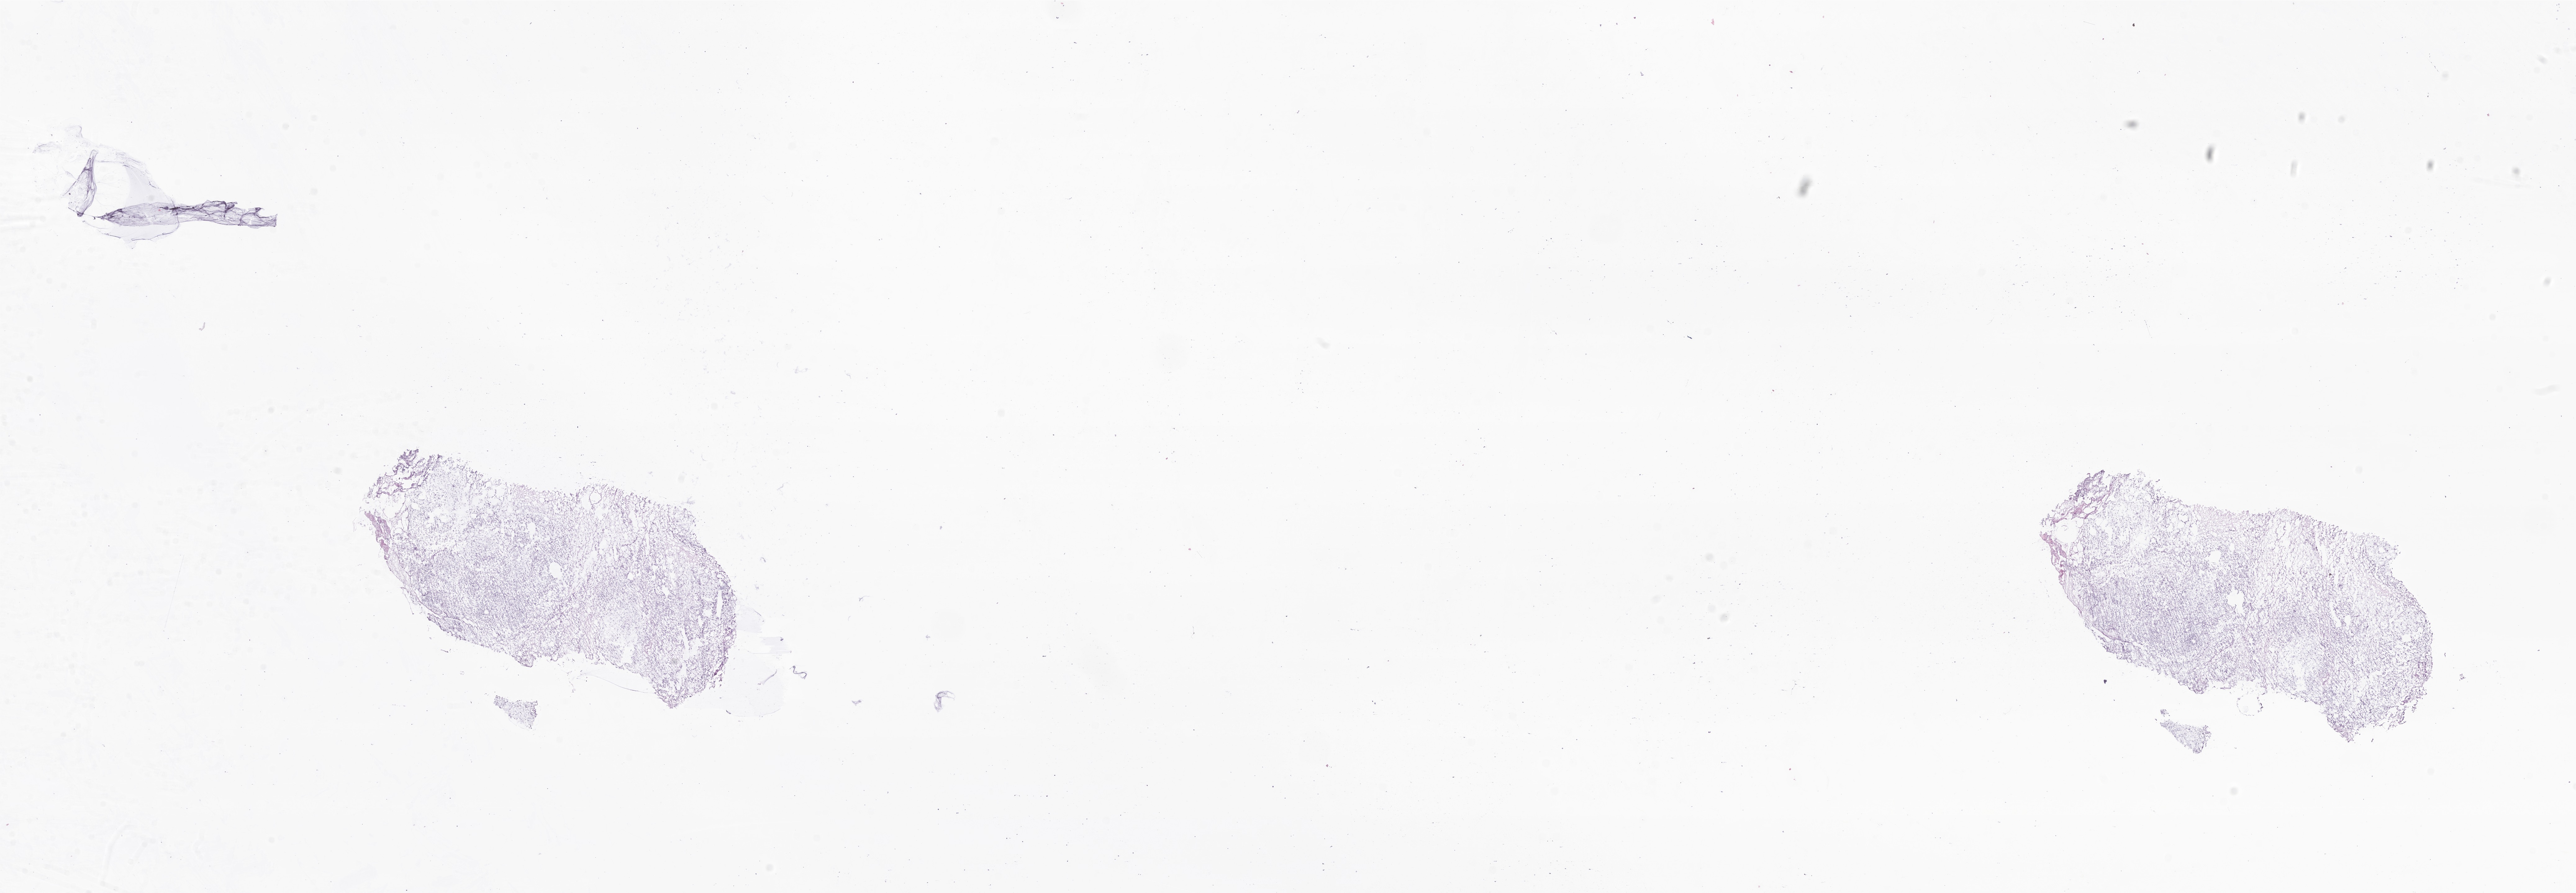
Digitized haematoxylin and eosin-stained section of tumor tissue from the brain, shown as a low-resolution overview of the whole scanned area (about 35.0 x 12.1 mm). Frozen section. Patient: female, age 99 months (8 years 3 months).
Recorded diagnosis: Mixed germ cell tumor.